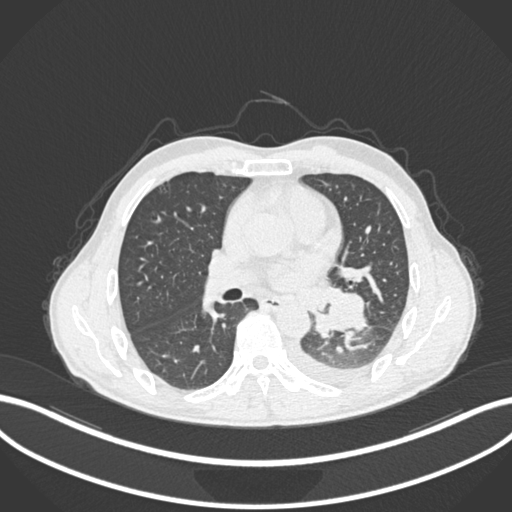
Chest CT, one axial slice; slice 129 of 222 in the series (ordered by position); lung window (W 1500 / L -600 HU); 512 × 512 image matrix, field of view 400 × 400 mm. Male patient, age 47 years. Case-level facts recorded for this patient, not image findings: clinical TNM (as recorded): T3 N1 M1c; histopathological grade: G3.
Structures marked on this image (rectangle marked by the reading radiologist):
- lung tumour (recorded histology: small cell carcinoma): bounding box [x1, y1, x2, y2] px = [310, 287, 370, 338]